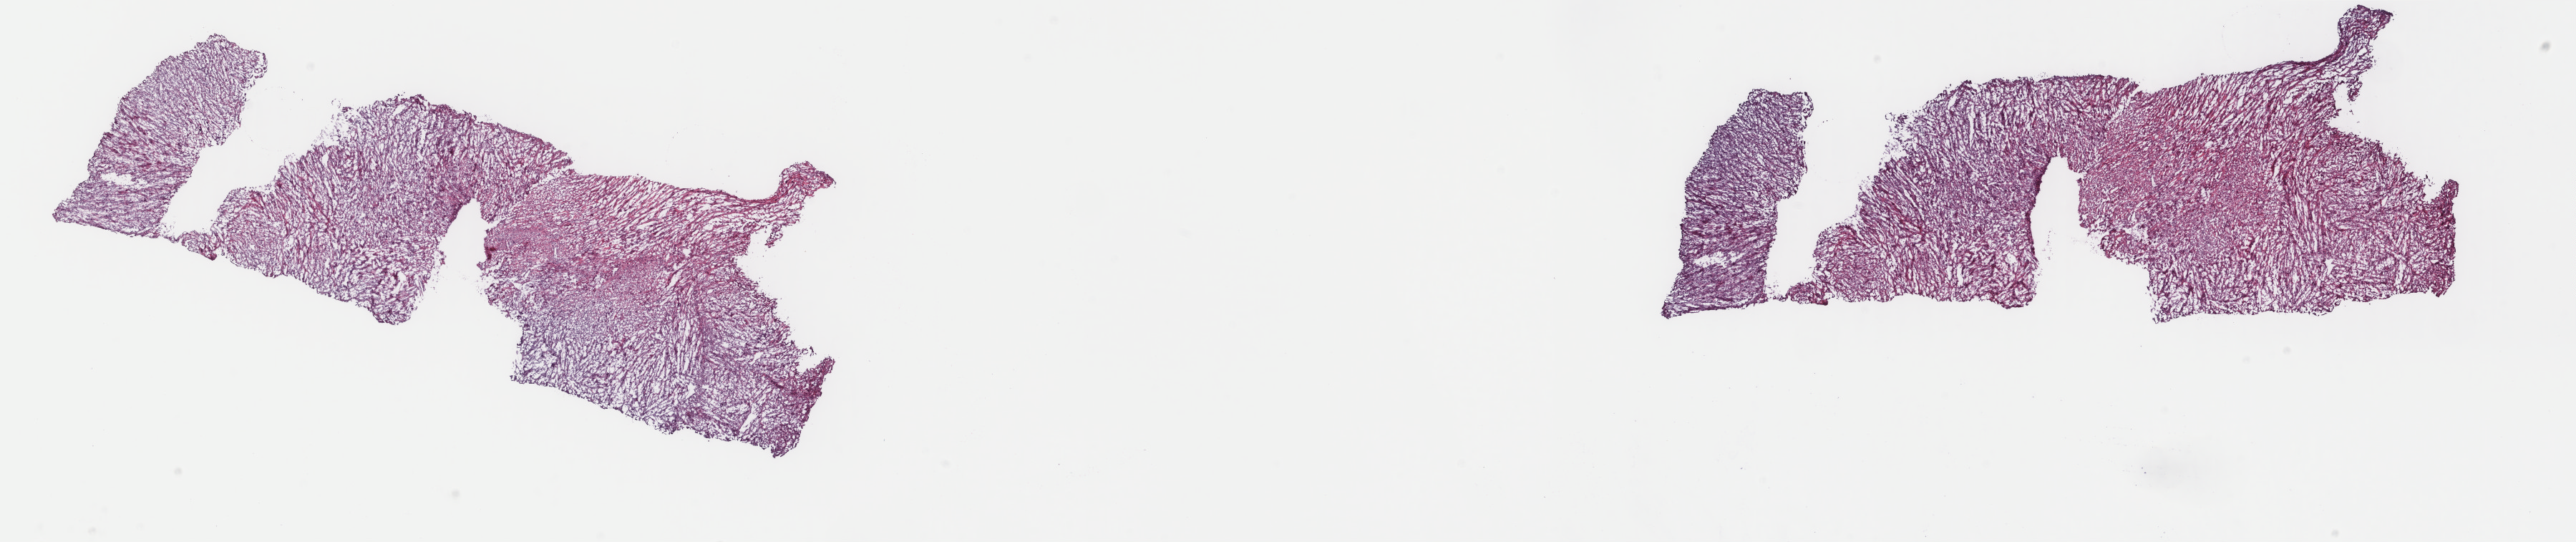
Whole-slide histology image, H&E-stained — shown as a low-resolution overview of the whole scanned area (about 28.6 x 6.0 mm). Frozen section from the top of the tissue portion. Uterus, primary tumour sample. Patient: female, age at initial diagnosis 59 years. Slide review estimates, as recorded: tumour cells 80%, tumour nuclei 90%, normal cells 0%, stromal cells 10%, necrosis 10%. Infiltration values recorded for this section: lymphocyte infiltration 5%, monocyte infiltration 1%, neutrophil infiltration 0%.
Pathologic diagnosis: Leiomyosarcoma, NOS.